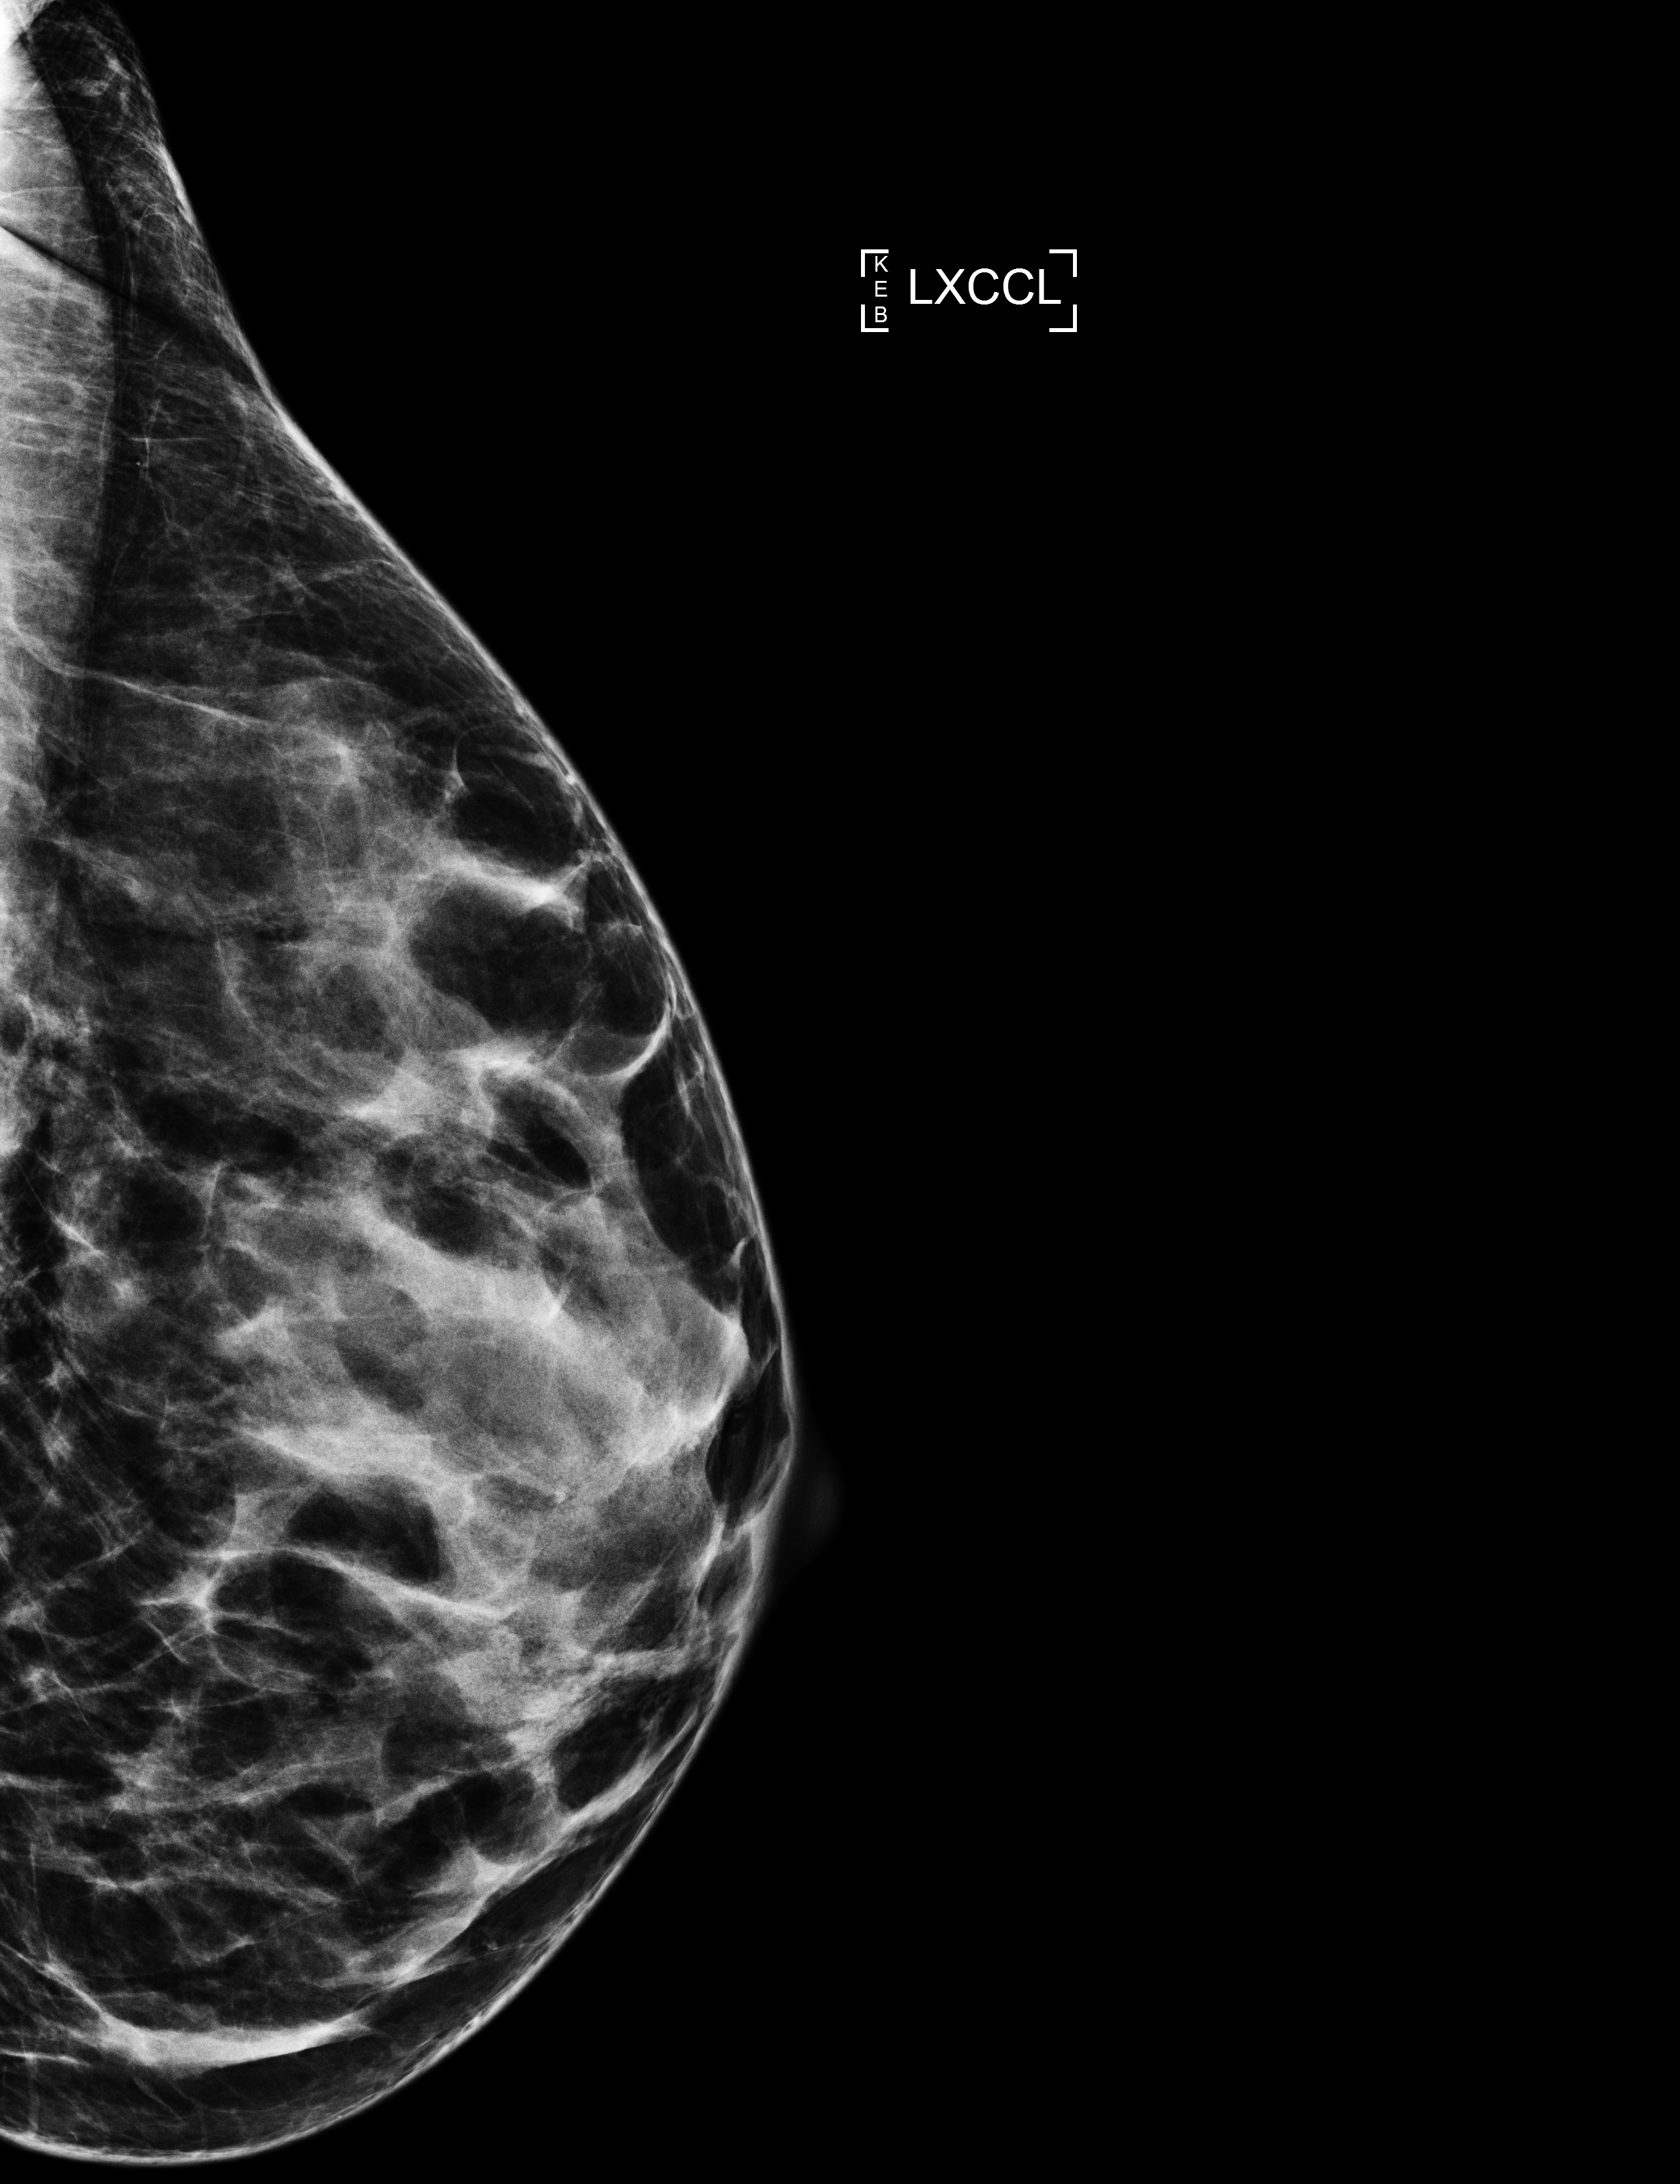
Diagnostic work-up study; compressed breast thickness 46 mm. Patient: female, 56 years.
Image type: full-field digital mammogram. Breast: left. Projection: exaggerated CC view (lateral).